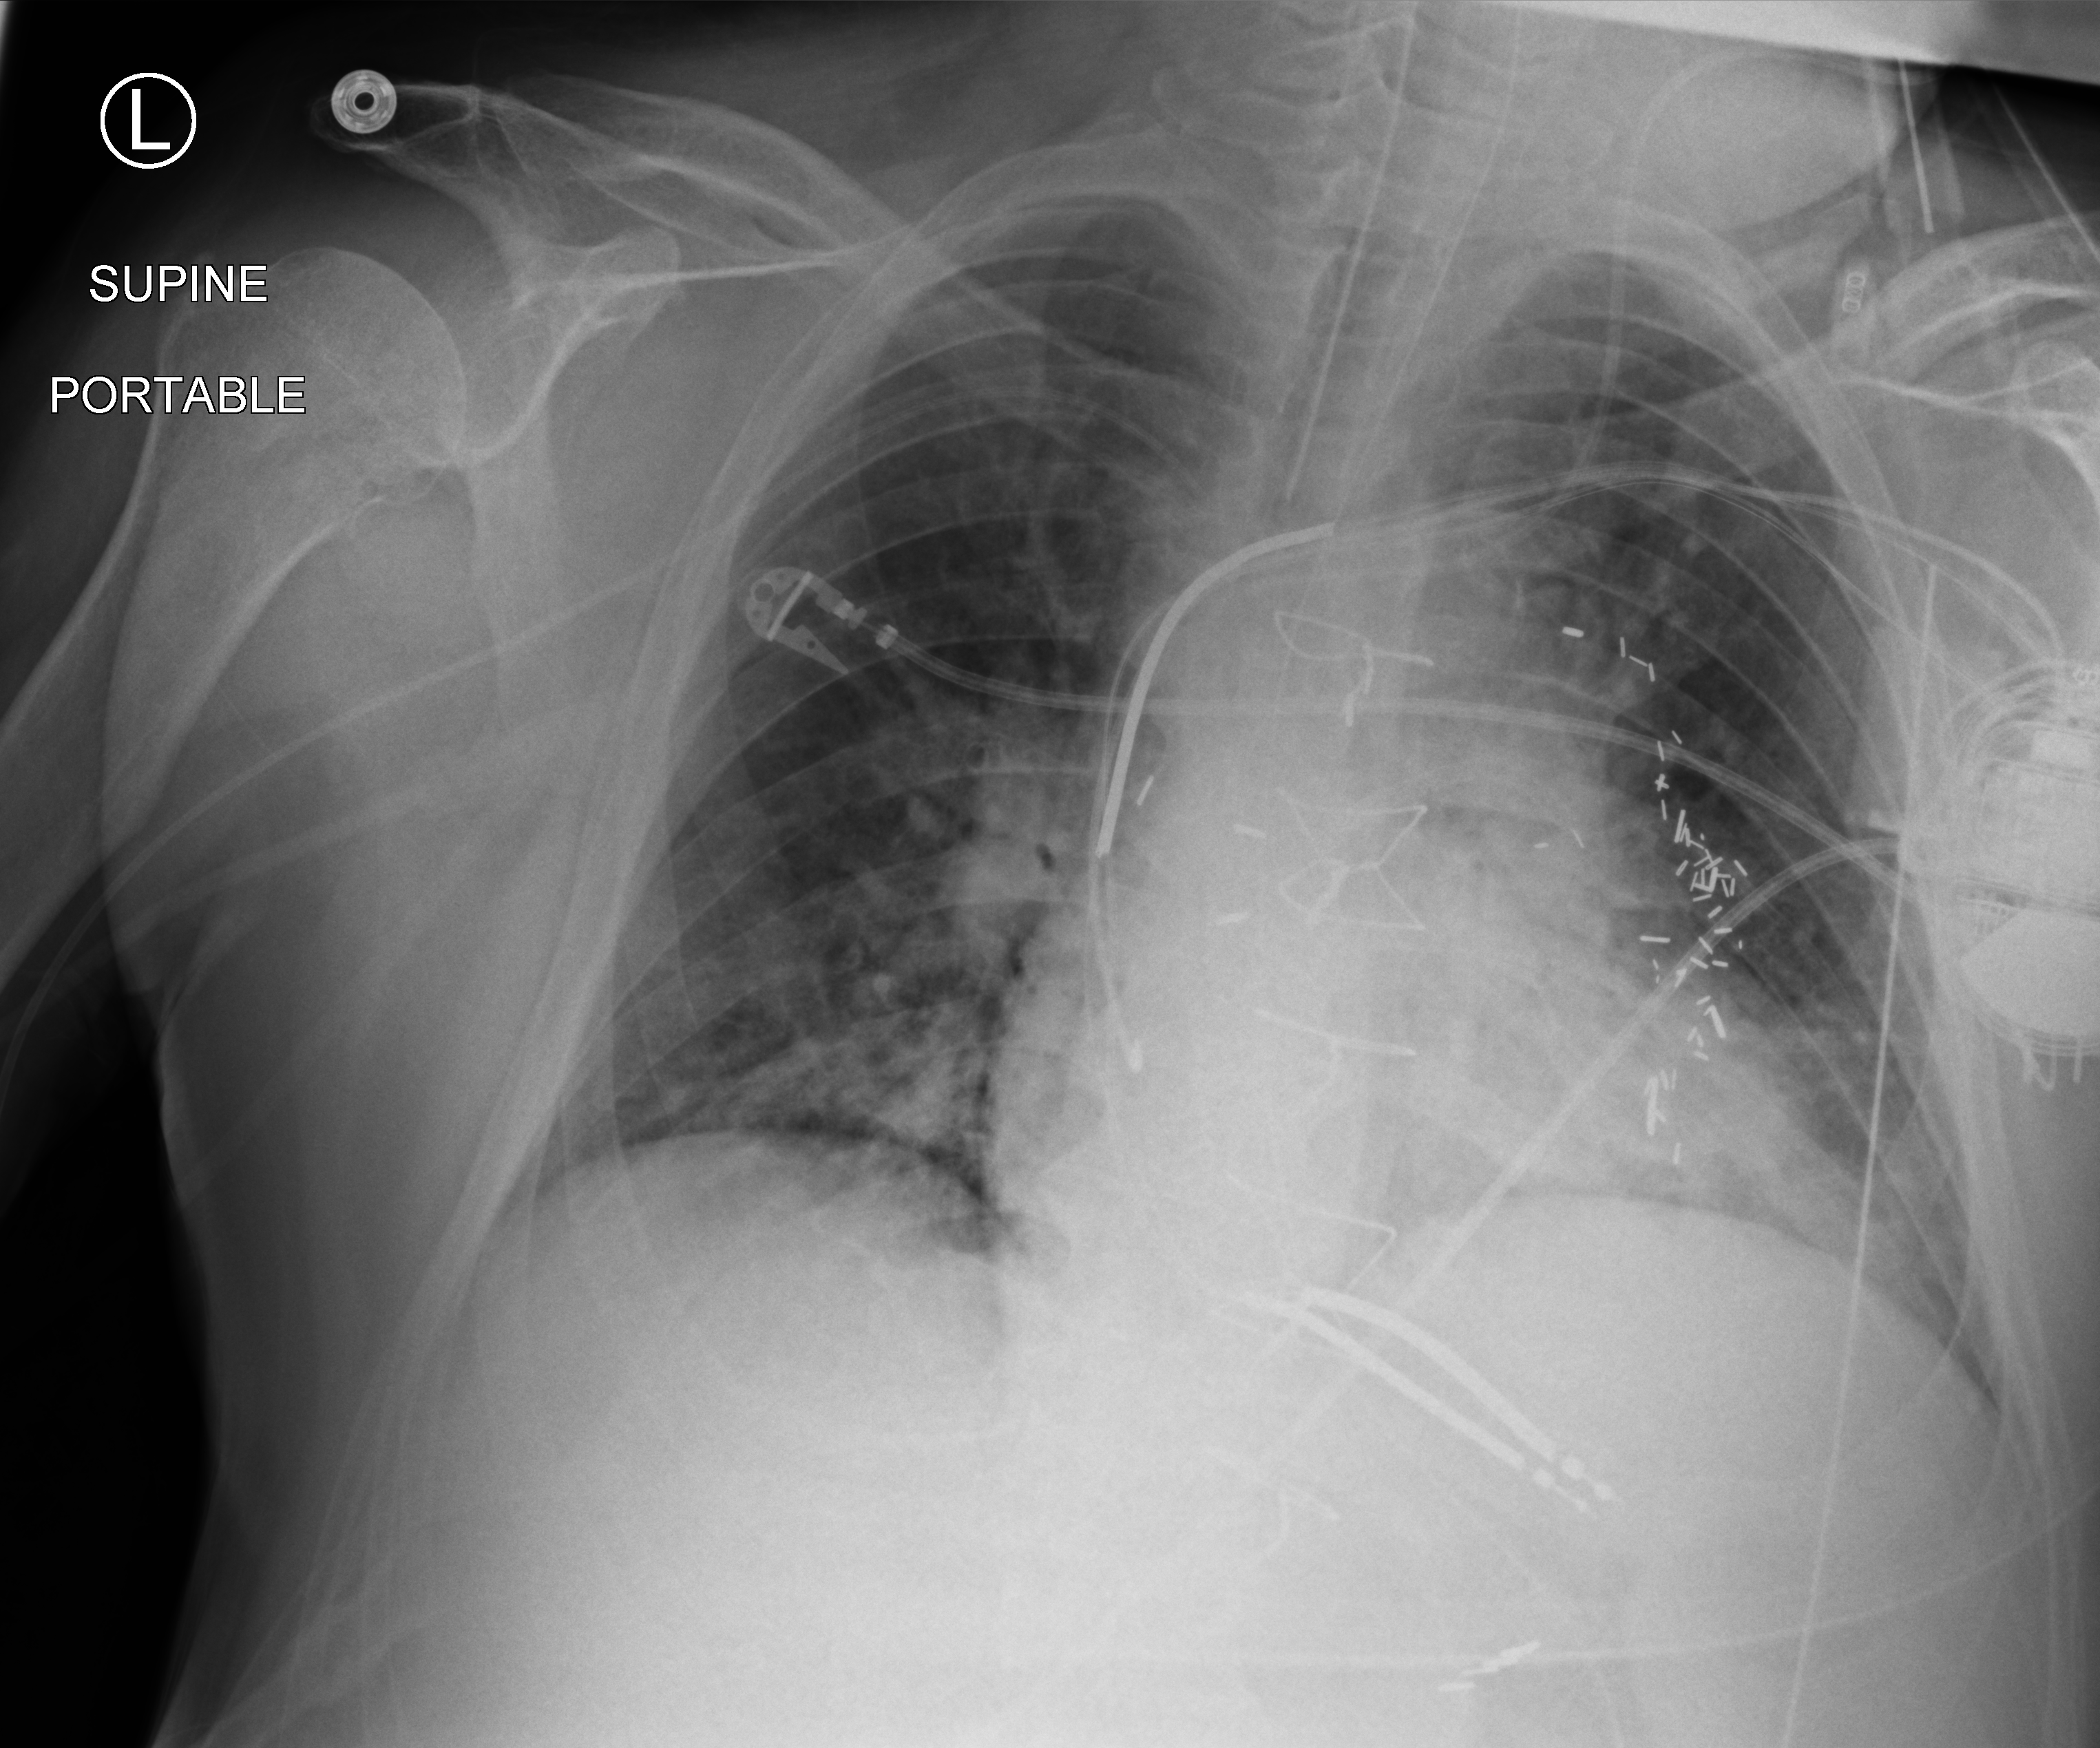
Portable chest radiograph; anteroposterior (AP) projection. Patient hospitalised with COVID-19; male, aged 60–74 years.
Hospital-stay facts (about this admission, not read from this image; timing relative to this image not recorded): mechanically ventilated during this hospital stay: yes; length of hospital stay: 55 days.